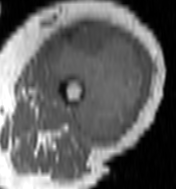
MRI of an extremity soft-tissue mass, one axial slice; slice 53 of 100 in the series (ordered by position); MR volume resampled by the dataset authors to the PET/CT grid (not the native acquisition matrix); 3.27 mm slice thickness; 176 × 189 image matrix, field of view 172 × 185 mm. Female patient. Case-level facts recorded for this patient, not image findings: histological type: undifferentiated – high grade; grade: high; site of the primary tumour: left thigh.
Annotated regions visible in this slice (expert contour drawn on MRI and transferred to this co-registered scan by the dataset authors):
- gross tumour volume including surrounding oedema: bounding box [x1, y1, x2, y2] px = [50, 25, 145, 143]
- gross tumour volume (mass): [50, 25, 145, 143]